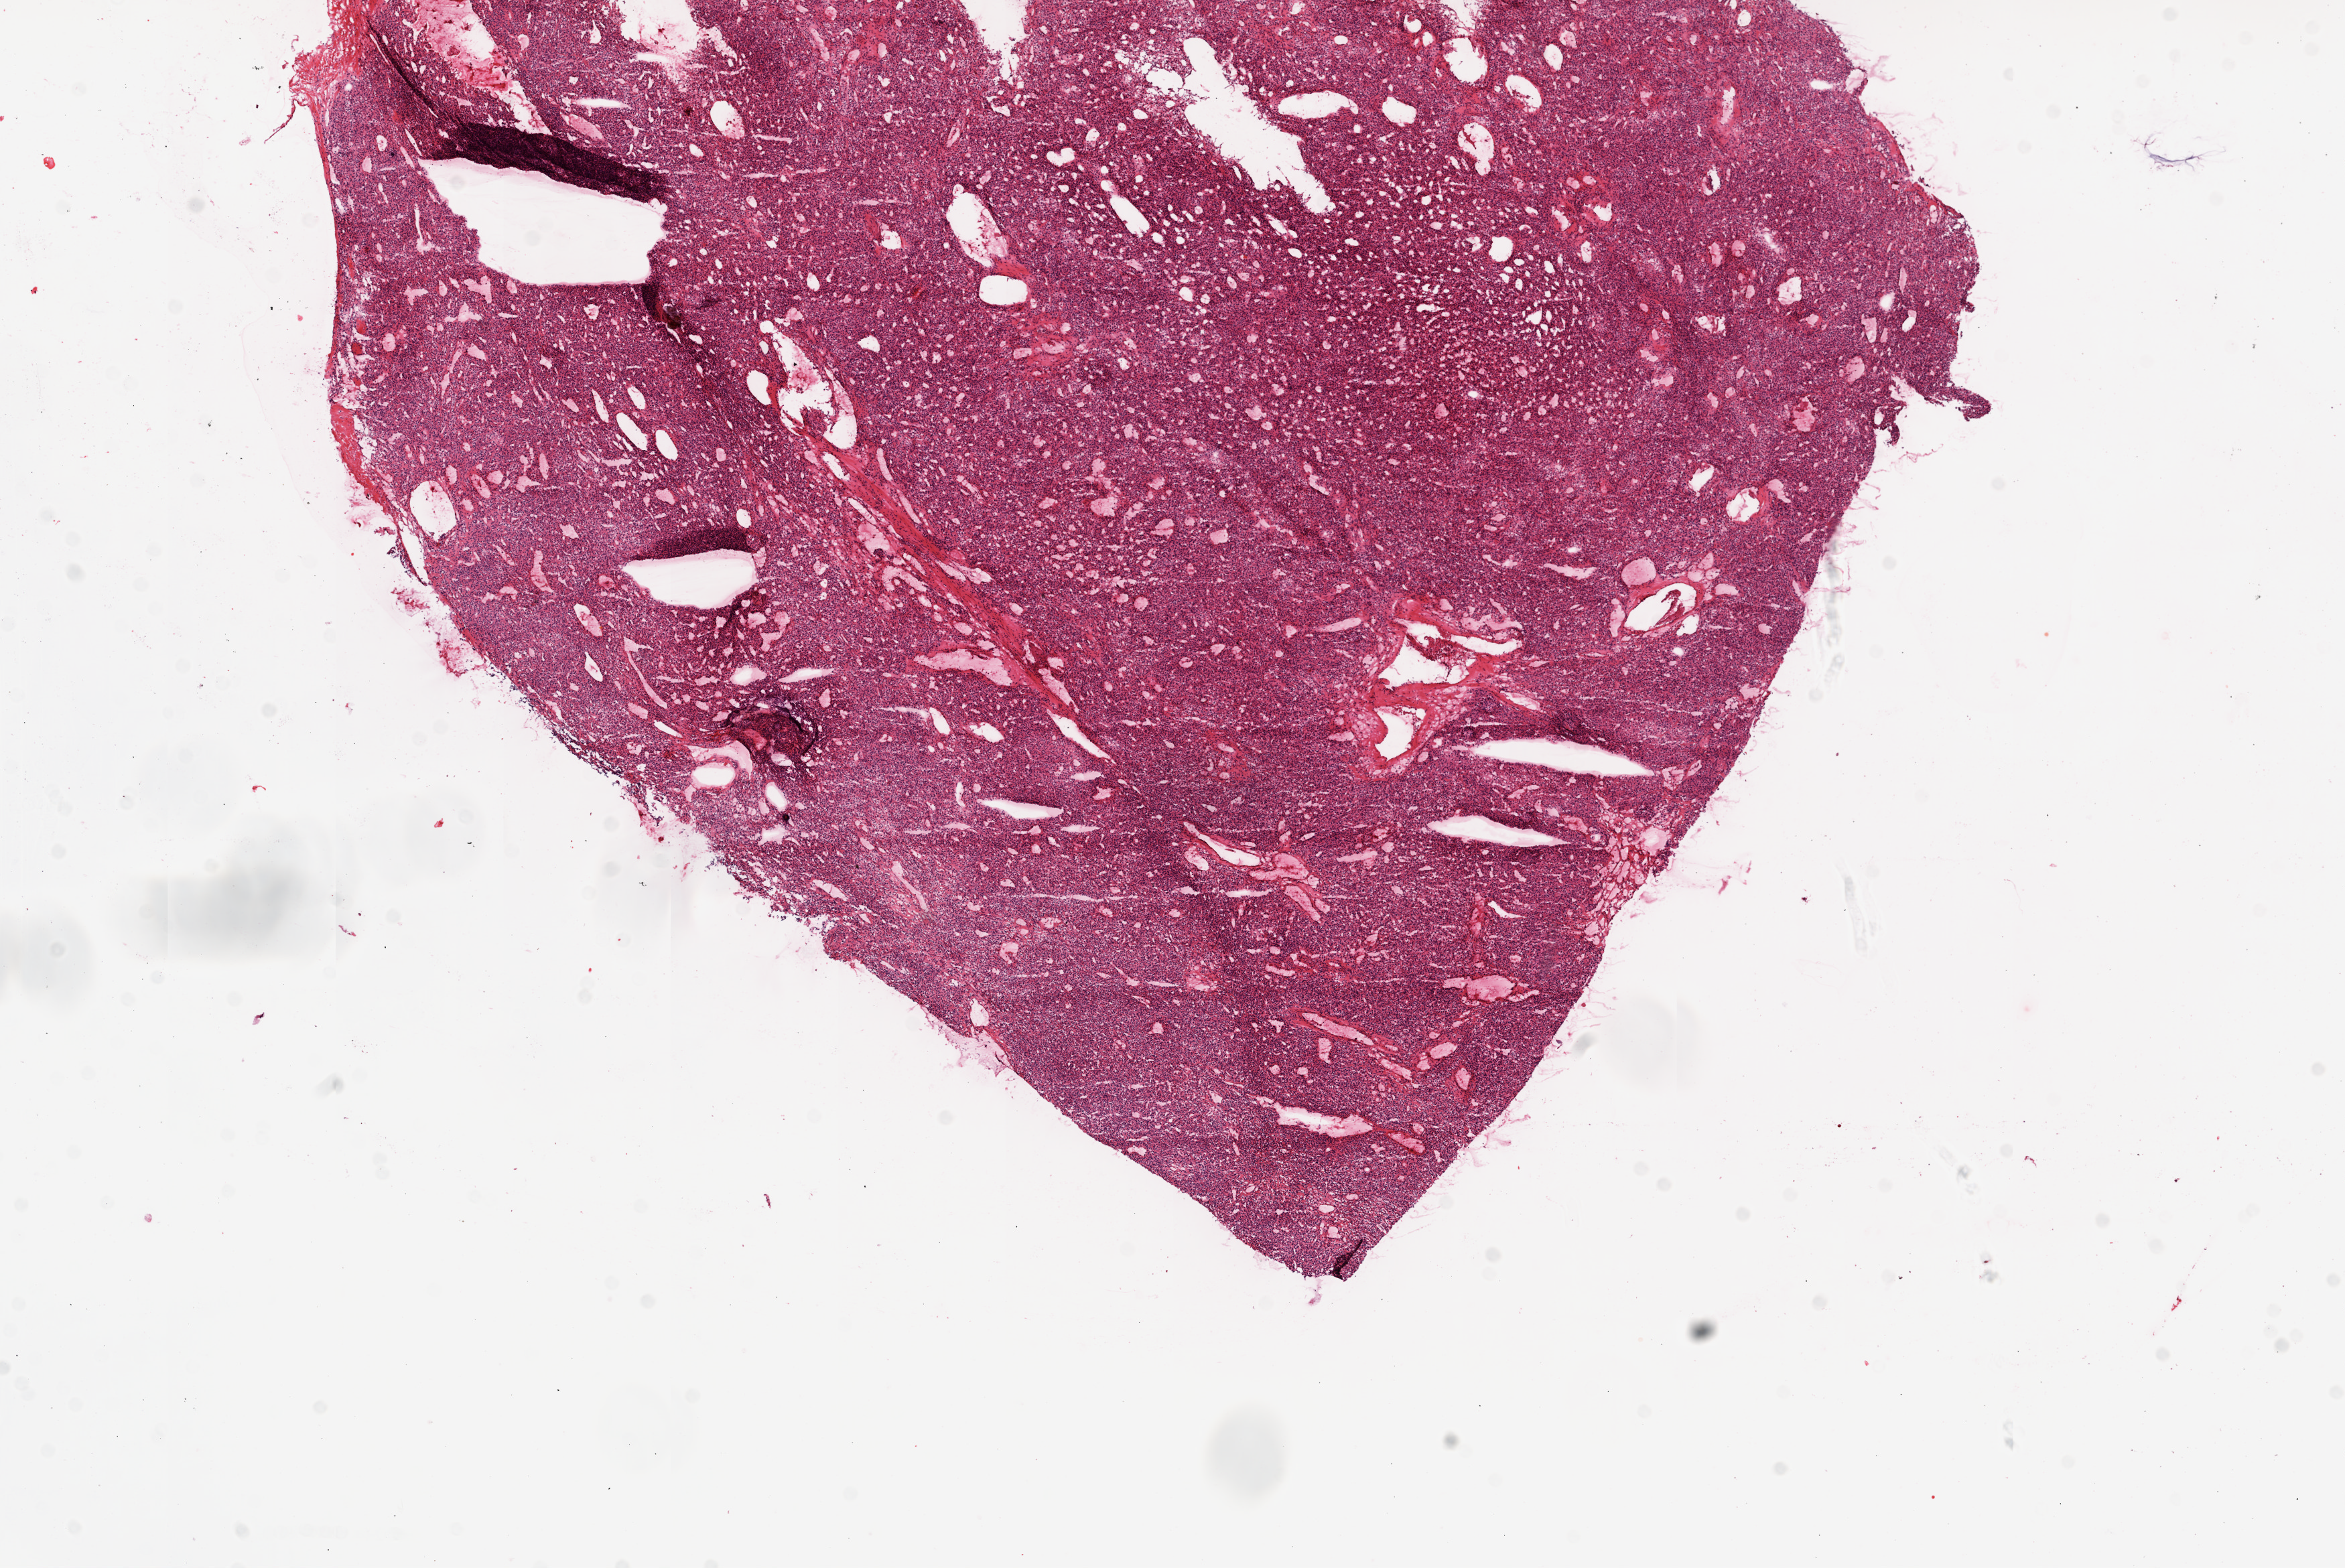
Whole-slide histology image, H&E-stained — shown as a low-resolution overview of the whole scanned area (about 14.0 x 9.4 mm, from a 20x scan); frozen section from the top of the tissue portion; primary tumour sample from the kidney. Male, age 51 years at initial diagnosis. Histologic grade: G3 (poorly differentiated). Slide review estimates, as recorded: tumour cells 95%, tumour nuclei 90%, normal cells 0%, stromal cells 5%, necrosis 0%.
AJCC pathologic stage: III. Diagnosis: Clear cell adenocarcinoma, NOS. TNM: T3a NX M0.